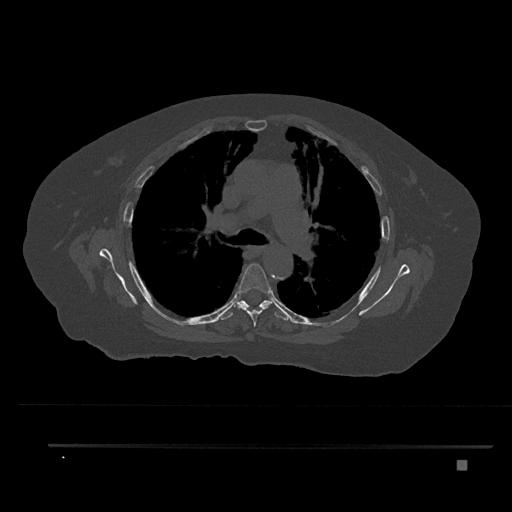
CT including the spine, one axial slice; position 553 of 797 along the scan axis; 120 kVp; bone window (W 1800 / L 400 HU); 0.5 mm slice thickness; 512 × 512 image matrix, field of view 437 × 437 mm. Patient: female, 76 years. Case-level facts recorded for this patient, not image findings: primary cancer: lung; vertebrae with lytic lesions (as recorded): T11, L3.
Structures marked on this image (semi-automatically segmented with operator editing):
- T5 vertebra: bounding box [x1, y1, x2, y2] px = [234, 263, 274, 327]
- T6 vertebra: [219, 300, 290, 321]